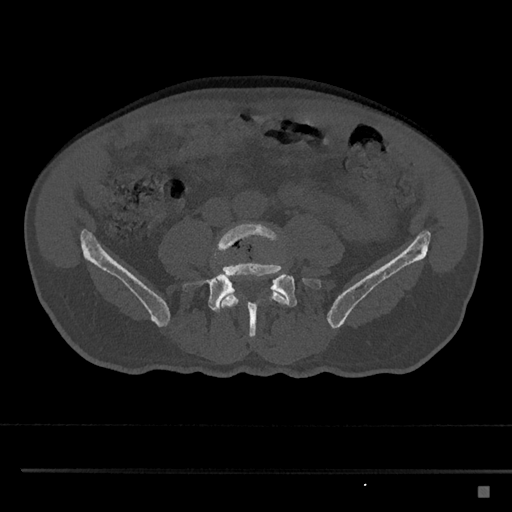
CT including the spine, one axial slice; slice 603 of 797 in the series (ordered by position); reconstruction kernel Br40s/3; bone window (W 1800 / L 400 HU); 0.5 mm slice thickness; 512 × 512 image matrix, field of view 391 × 391 mm. Male patient, age 59 years. From the clinical record (not read from this slice): primary cancer: prostate.
Structures marked on this image (semi-automatically segmented with operator editing):
- L4 vertebra: bounding box (x1, y1, x2, y2) in pixels: (213, 222, 289, 319)
- L5 vertebra: (181, 254, 325, 340)